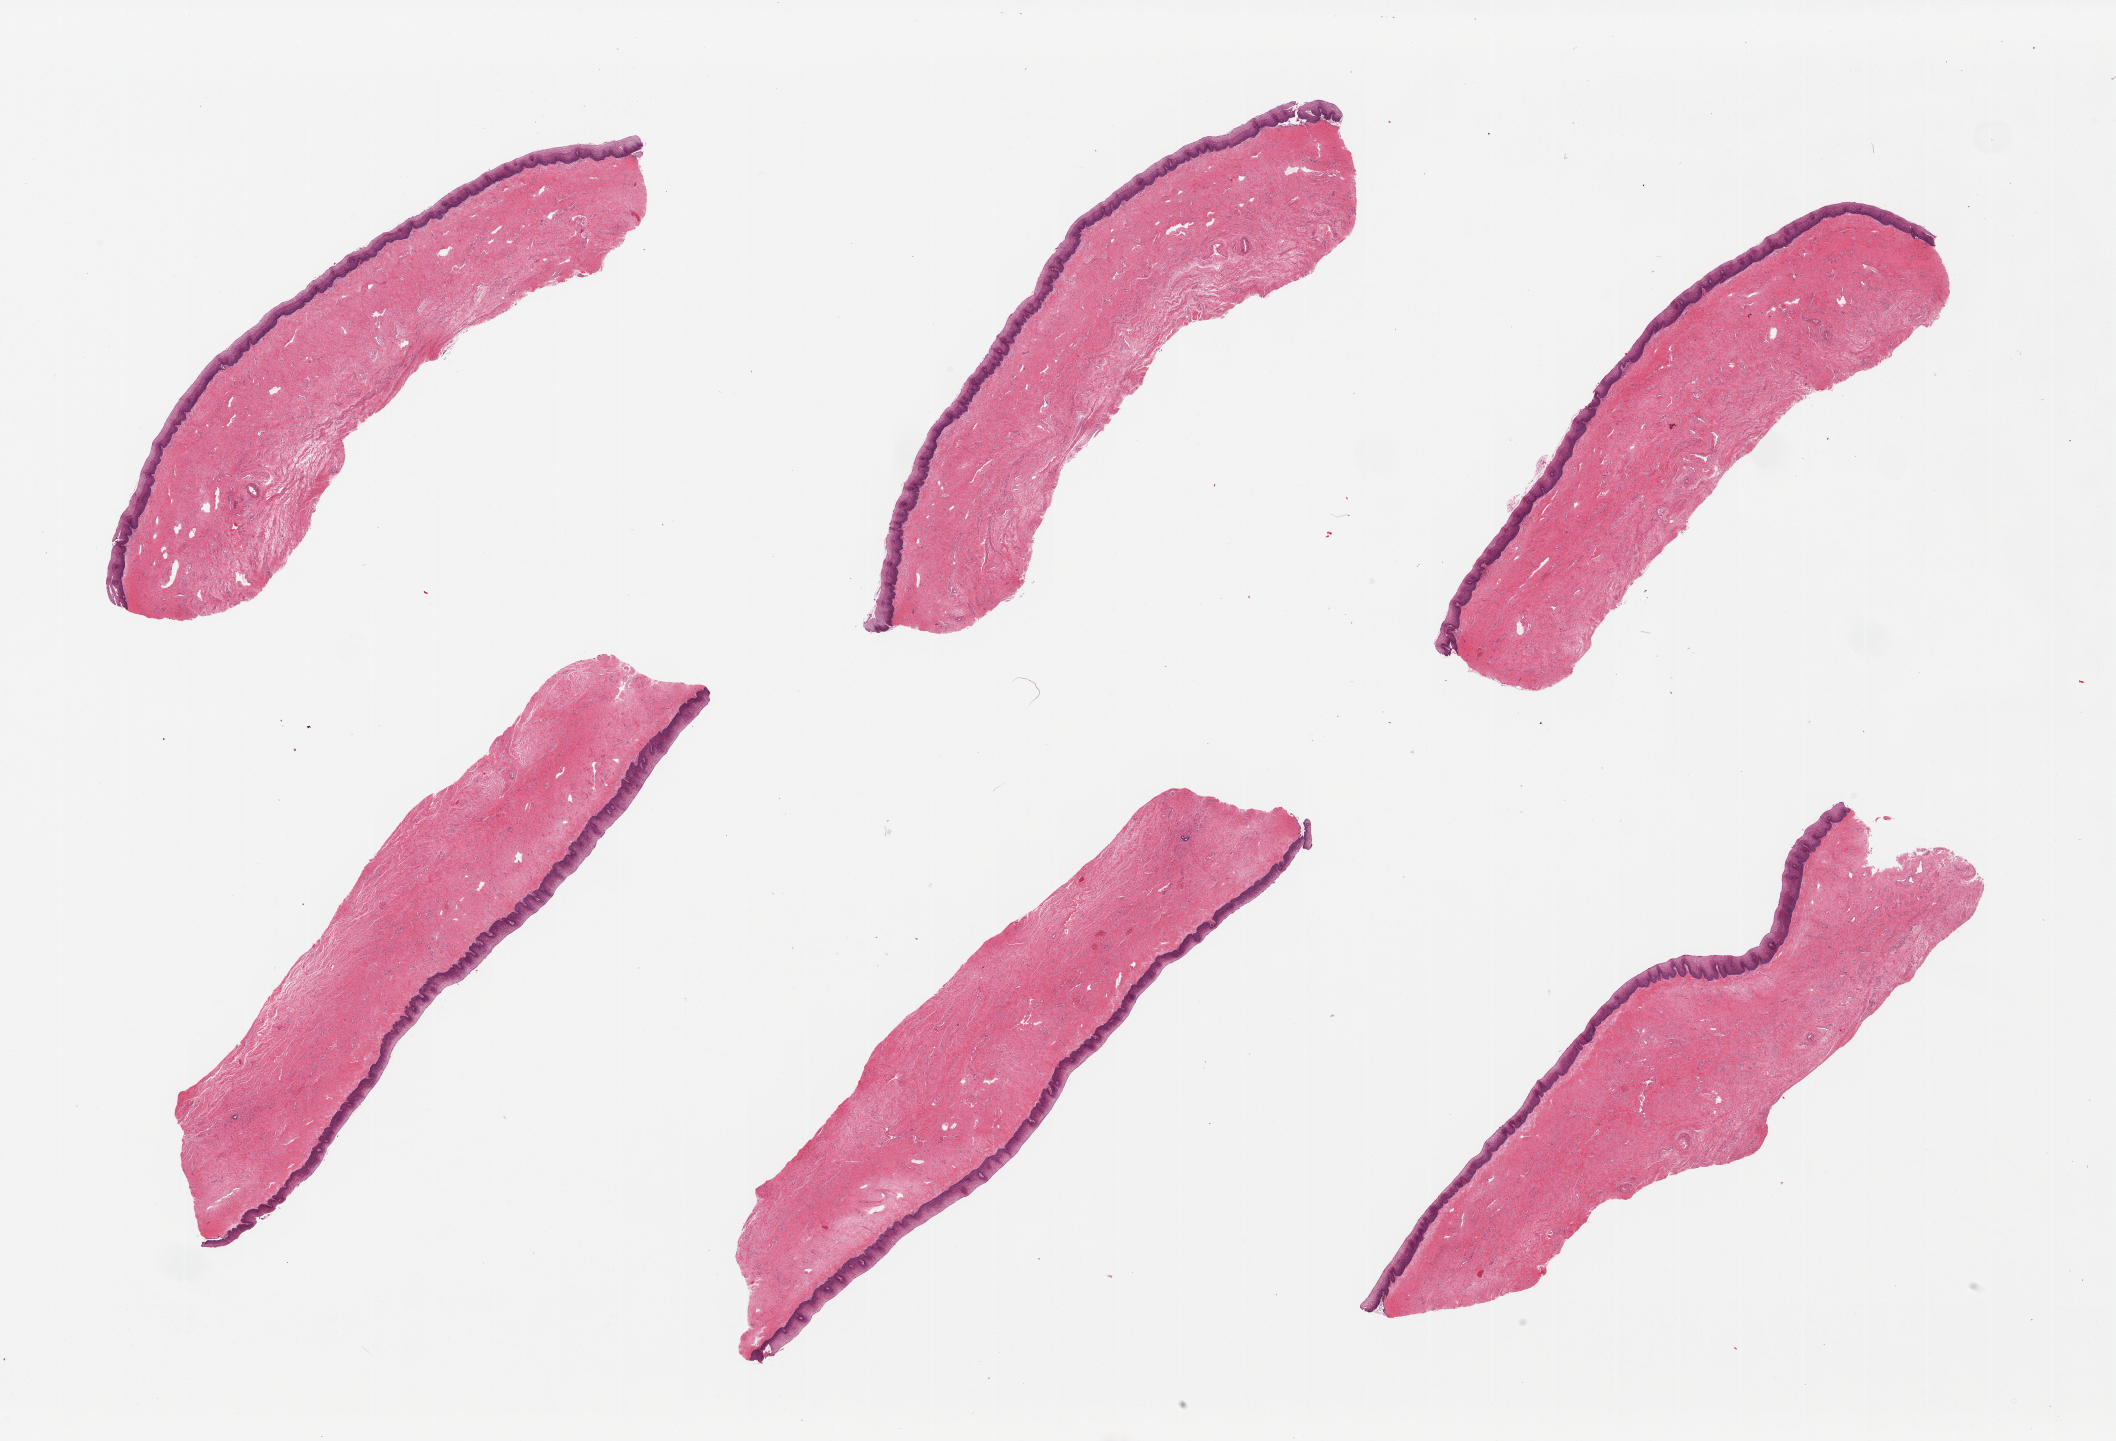
Haematoxylin and eosin whole-slide image — shown as a low-resolution overview of the whole scanned area (about 33.5 x 22.8 mm), PAXgene-fixed, paraffin-embedded tissue, target tissue: vagina, tissue donor sample.
- pathologist's review note for this sample: 6 pieces, squamous mucosa is ~0.25mm, evidence of repithelialization